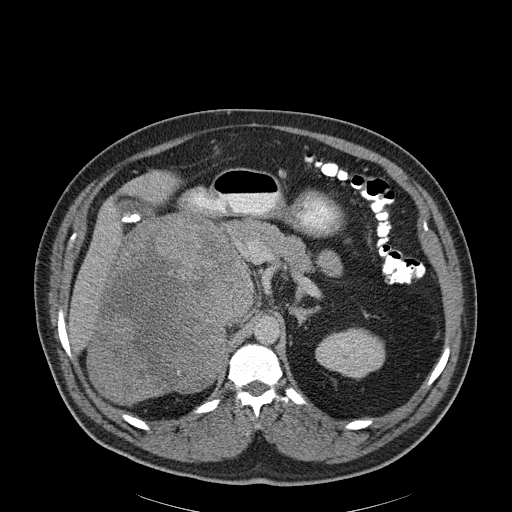
Contrast-enhanced abdominal CT, one axial slice. Slice 131 of 186 in the series (ordered by position). Reconstruction kernel B30f. Soft-tissue window (W 400 / L 40 HU). 3 mm slice thickness. 512 × 512 image matrix, field of view 464 × 464 mm. Male patient, age 56 years. Case-level facts recorded for this patient, not image findings: diagnosis: adrenocortical carcinoma; tumour side: right adrenal; tumour size at pathology: 18 cm; Ki-67 index: 2 %; stage (as recorded): 3.
Structures marked on this image (semi-automatic segmentation, software-assisted and operator-edited):
- mass: bounding box [x1, y1, x2, y2] px = [90, 215, 250, 403]